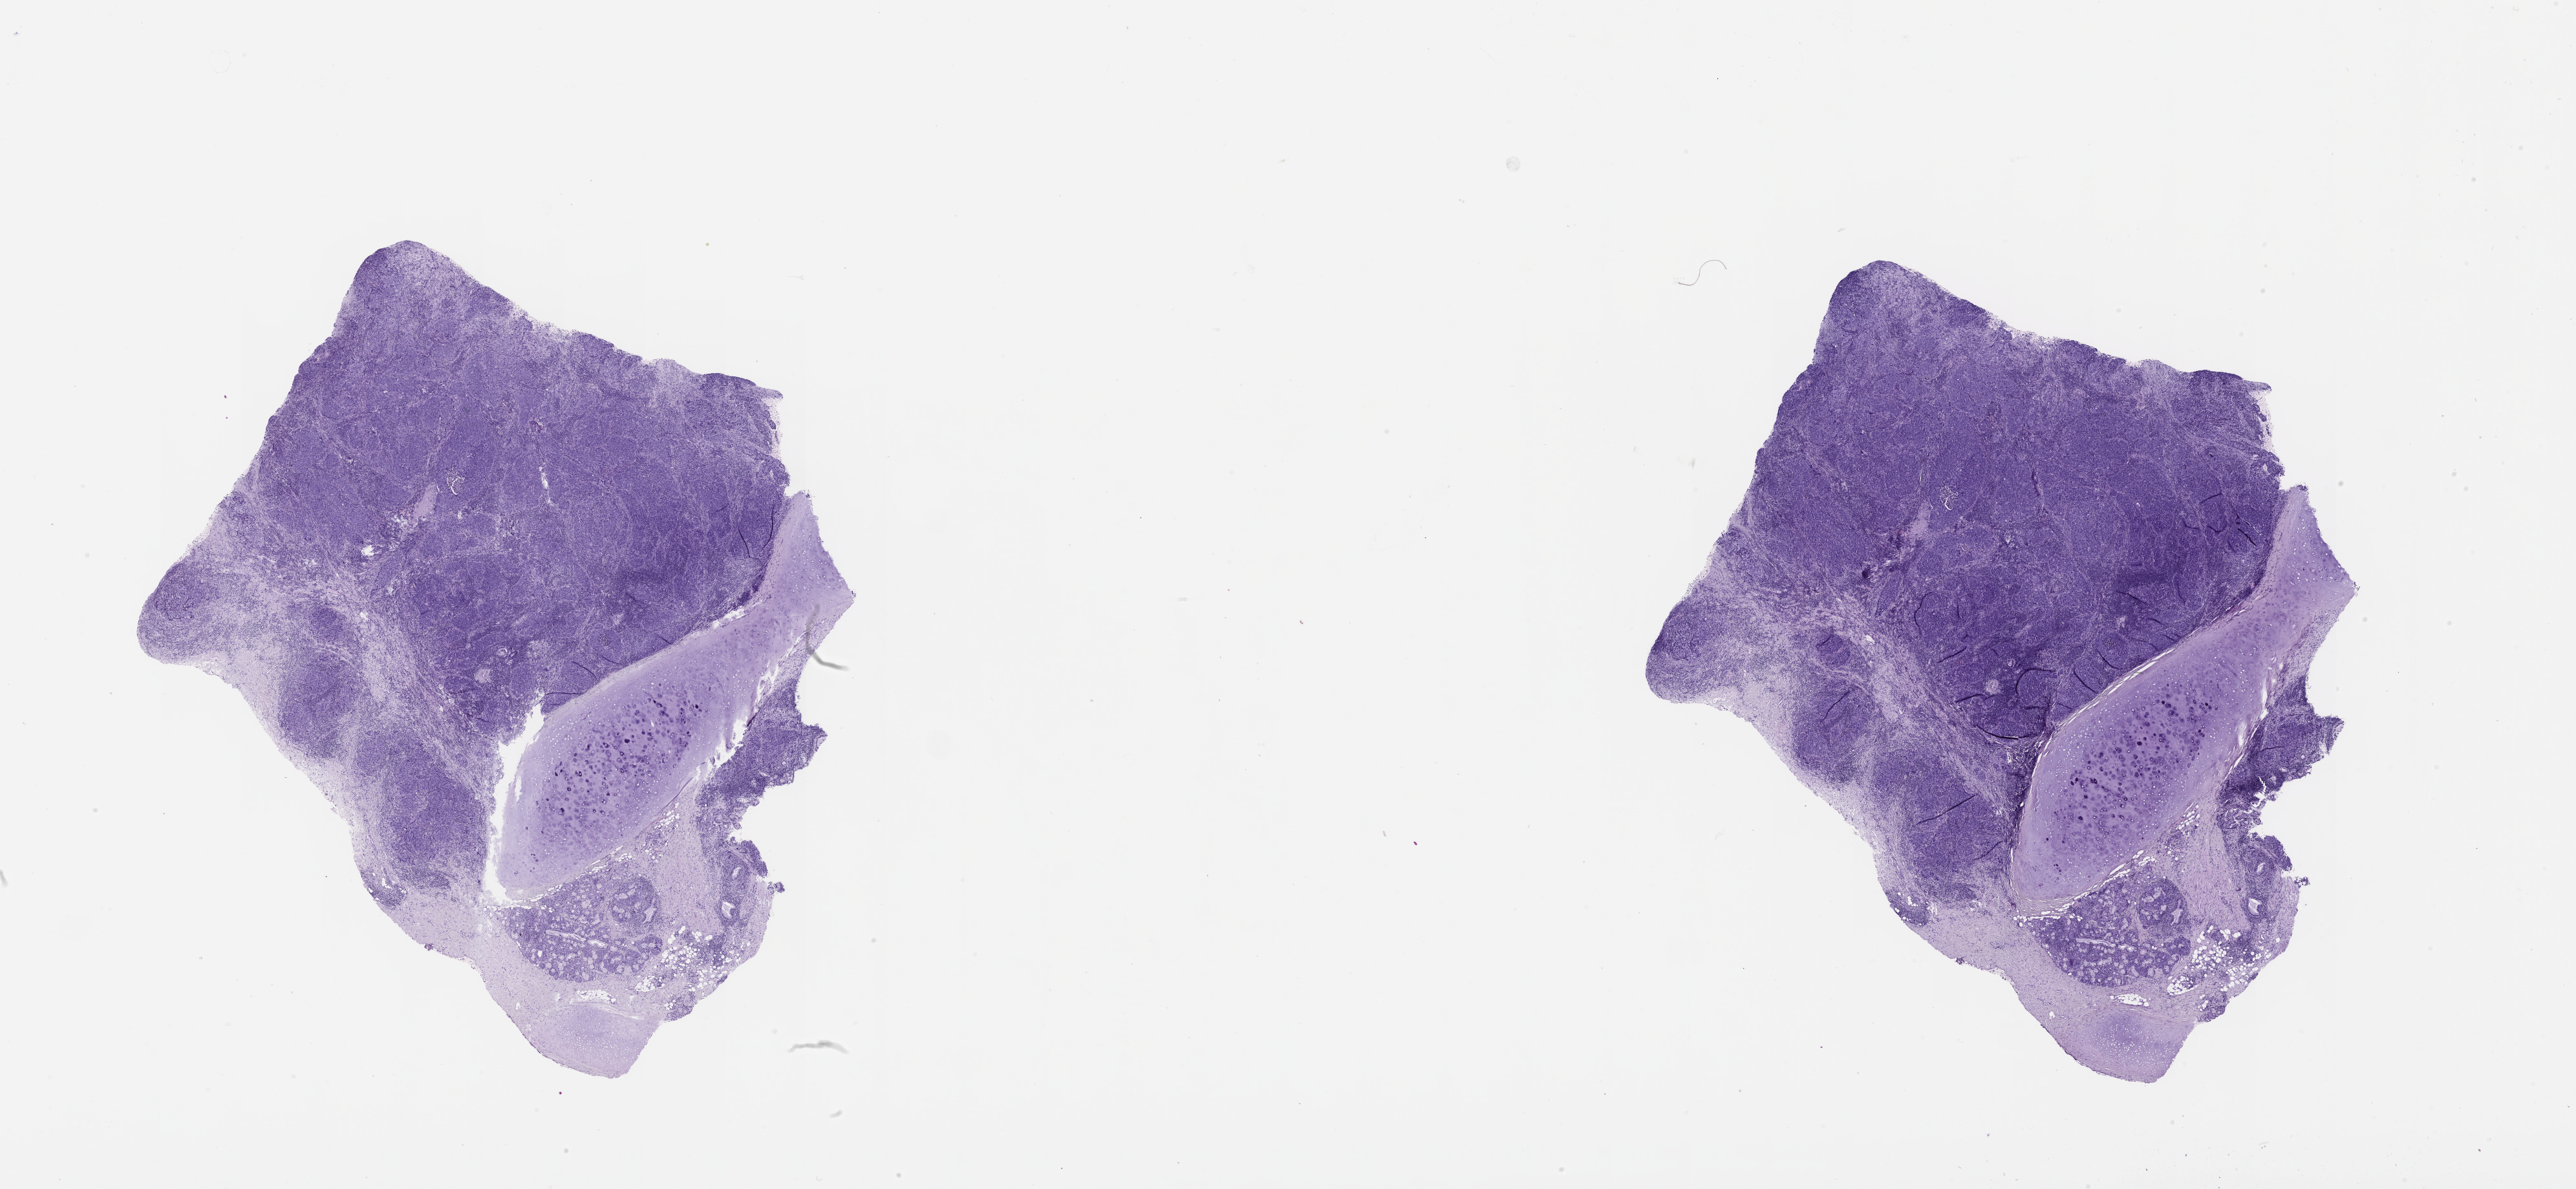
Digitized H&E tissue section (whole slide), shown as a low-resolution overview of the whole scanned area (about 32.1 x 14.8 mm), lung, tumour tissue. Patient: male, age 63 years.
• patient diagnosis (cohort enrolment): squamous cell carcinoma (lung)